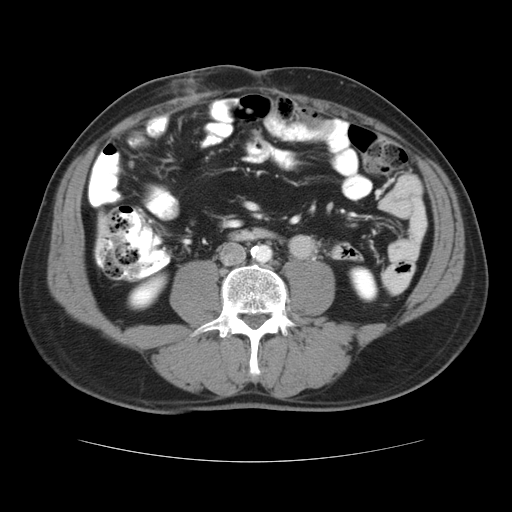
Contrast-enhanced abdominal CT, one axial slice; position 4 of 37 along the scan axis; 120 kVp; soft-tissue window (W 400 / L 40 HU); 5 mm slice thickness; 512 × 512 image matrix. Male patient, age 66 years. From the clinical record (not read from this slice): diagnosis: colorectal cancer liver metastases, imaged before liver resection; multiple liver metastases: yes; largest metastasis: 1.6 cm; disease in both lobes: yes.
Structures marked on this image (outlined manually by an expert reader):
- liver: bounding box [x1, y1, x2, y2] px = [98, 232, 107, 240]
- planned liver remnant (the part of the liver to remain after resection): [98, 229, 107, 257]